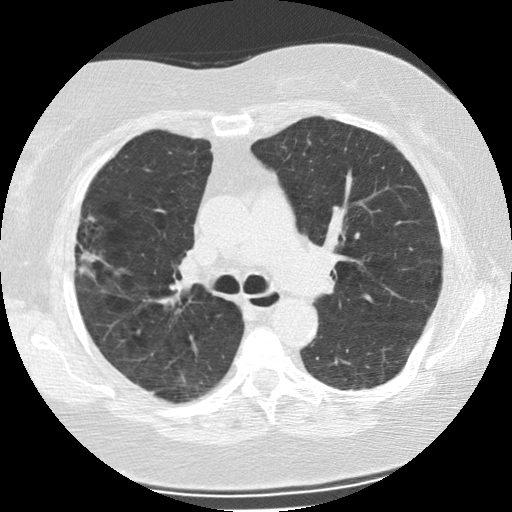
Chest CT (low-dose screening protocol), one axial image. Second screening round (one year after baseline). Lung window (W 1500 / L -600 HU). 512 × 512 image matrix, field of view 320 × 320 mm. Female, age 73 years at enrolment. Former smoker at enrolment.
- Expert reader's lesion annotation, box from (x=54, y=220) to (x=113, y=289) px.
- The screening reader recorded 2 non-calcified nodules or masses ≥4 mm on this exam (right upper lobe, left upper lobe); which of them this box marks is not recorded.
- Official screen result: positive, change unspecified: nodule(s) >= 4 mm or enlarging nodule(s), mass(es), or other non-specific abnormalities suspicious for lung cancer.
- Lung cancer was diagnosed 47 days after this screen: bronchiolo-alveolar adenocarcinoma, NOS, right upper lobe, moderately differentiated (G2), stage IIIB (AJCC 6th edition), 21 mm at pathology.